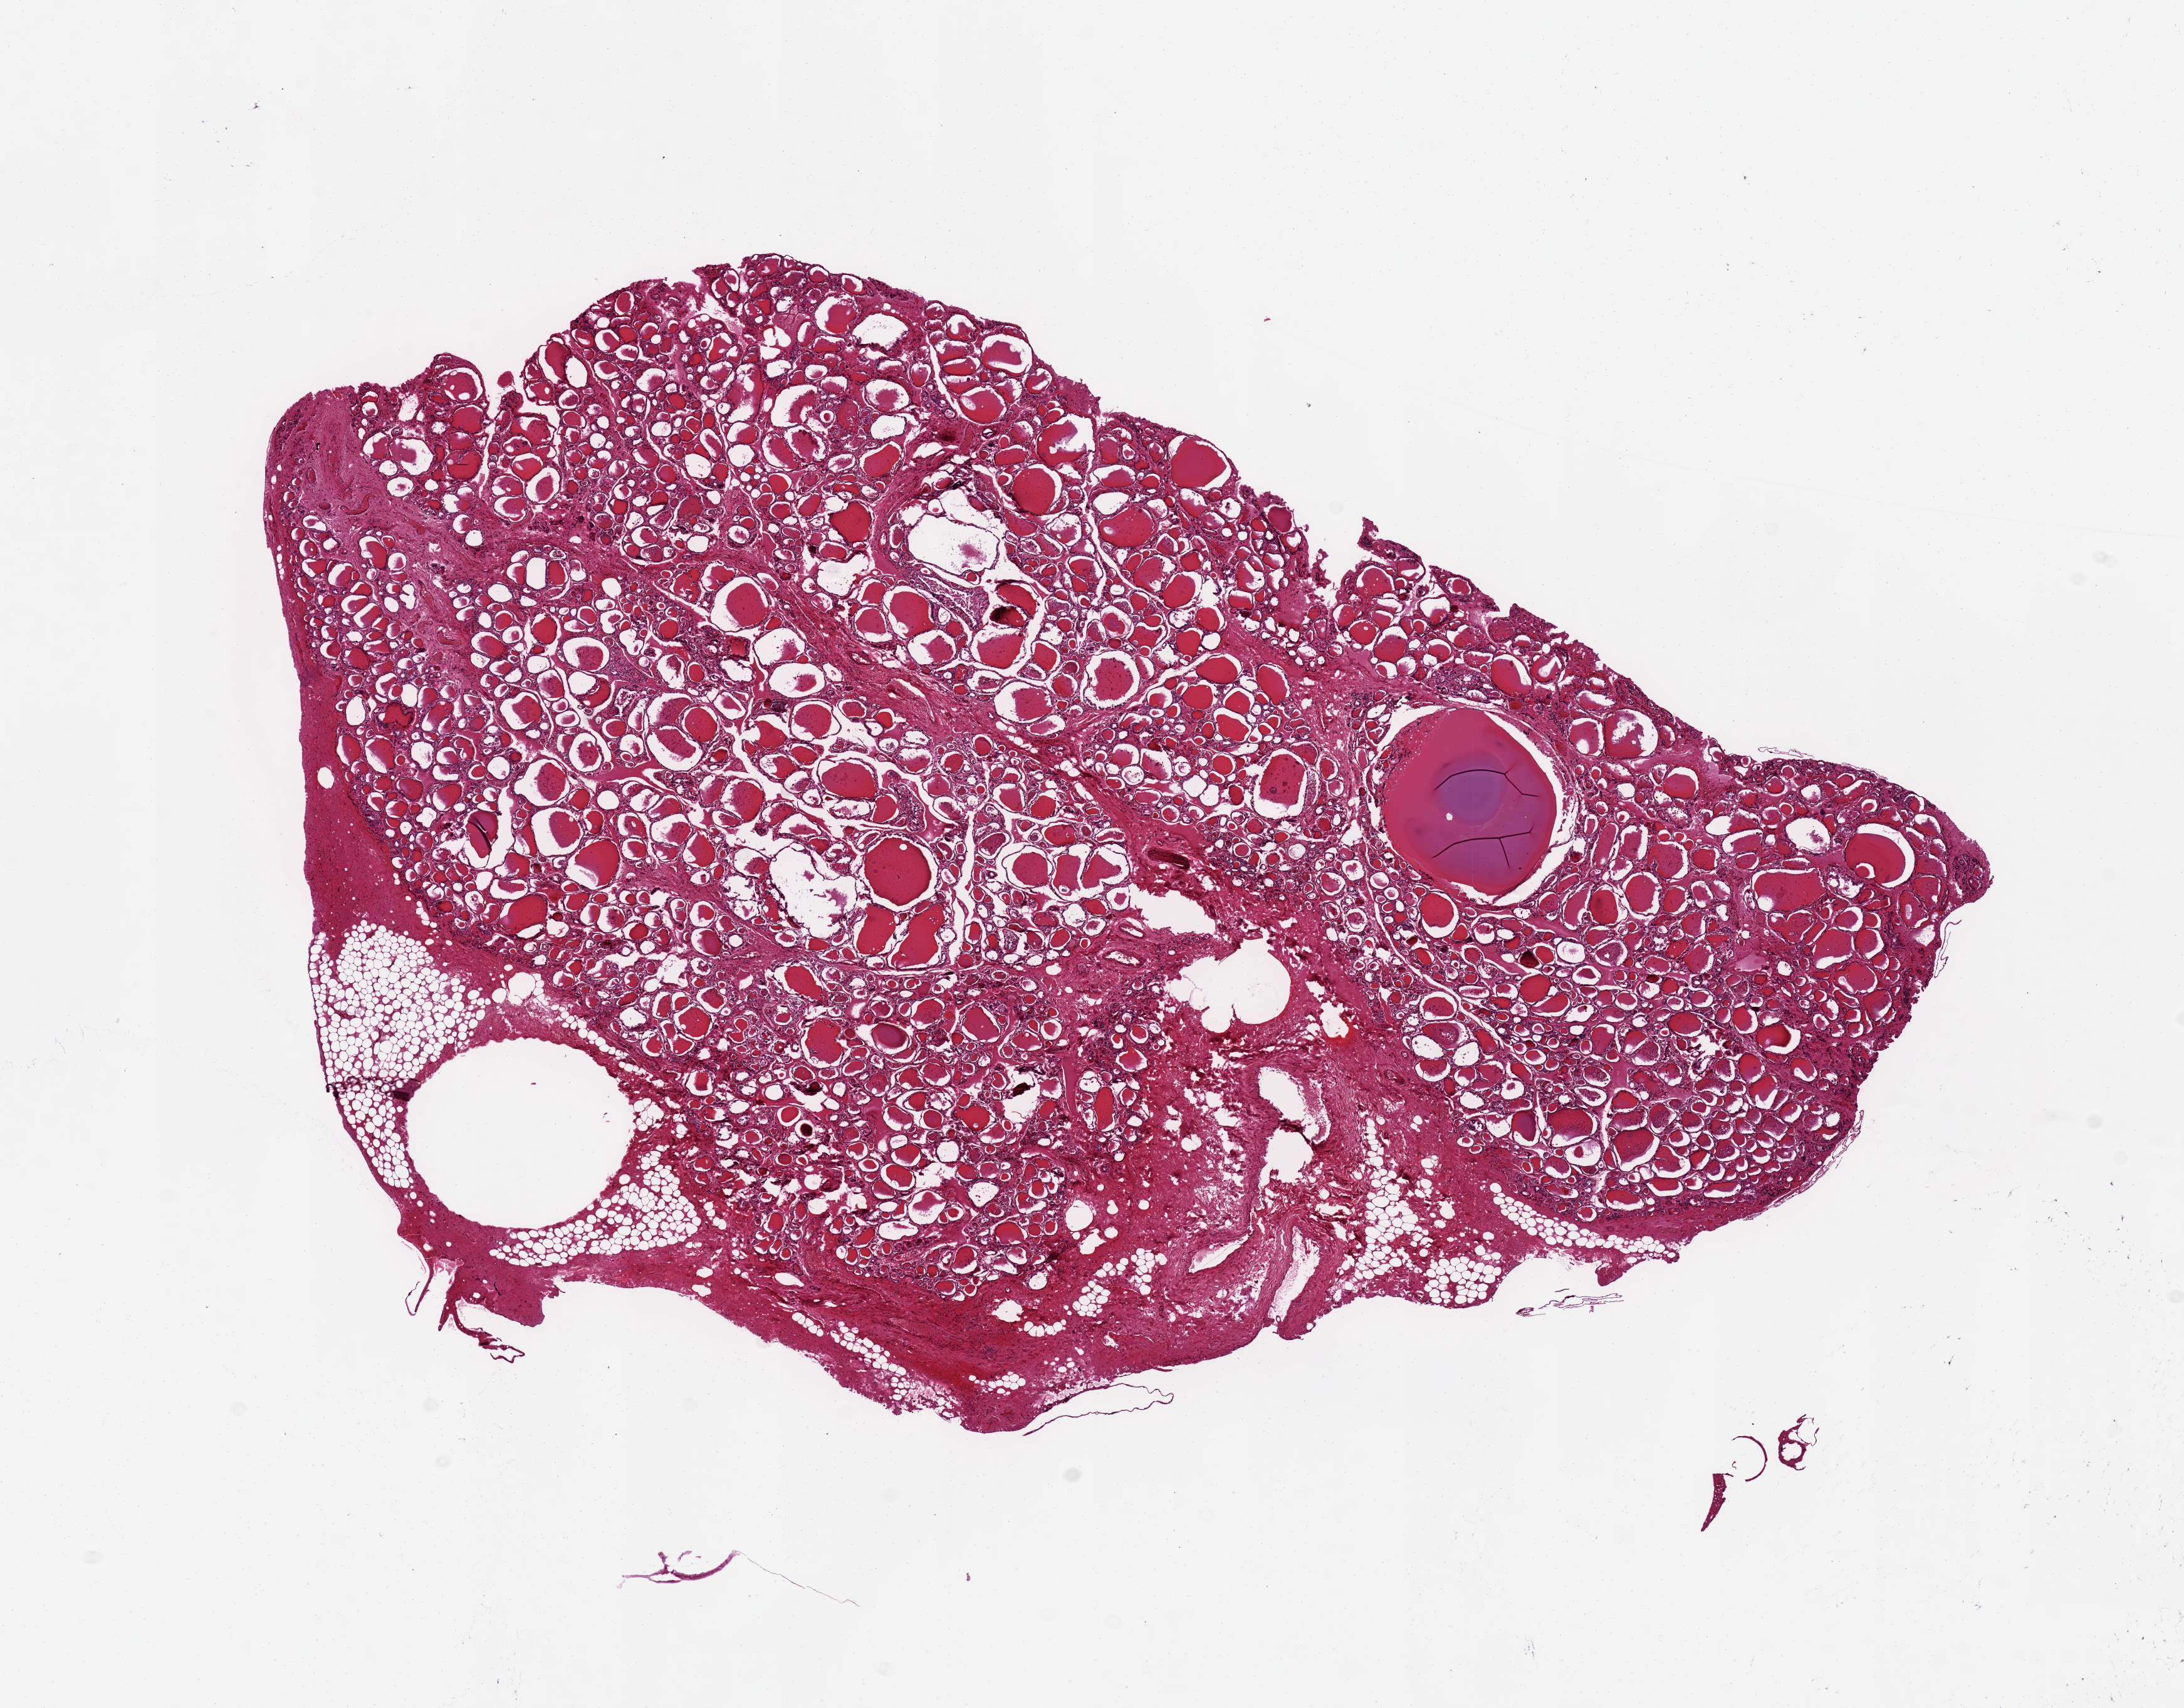
Hematoxylin and eosin (H&E) whole-slide image, shown as a low-resolution overview of the whole scanned area (about 13.8 x 10.8 mm), PAXgene-fixed, paraffin-embedded tissue, target tissue: thyroid, donor tissue sample. Female donor.
Review note (as recorded): Mild autolysis.